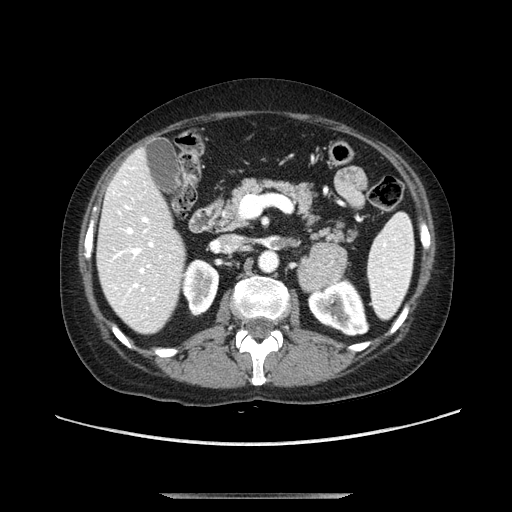
Contrast-enhanced abdominal CT, one axial slice; slice 56 of 107 in the series (ordered by position); soft-tissue window (W 400 / L 40 HU); 2.5 mm slice thickness; 512 × 512 image matrix, field of view 380 × 380 mm. Female patient. Case-level facts recorded for this patient, not image findings: diagnosis: adrenocortical carcinoma; tumour side: left adrenal; tumour size at pathology: 7.5 cm; Ki-67 index: 9 %; stage (as recorded): 3.
Outlined on this slice (semi-automatic segmentation, software-assisted and operator-edited):
- mass: bounding box (x1, y1, x2, y2) in pixels: (297, 243, 348, 292)